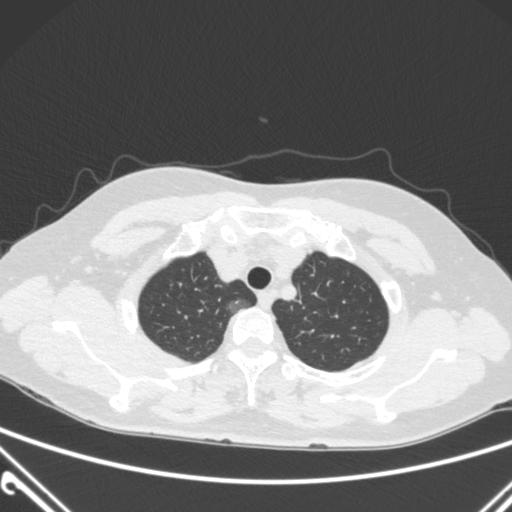
Chest CT, one axial slice. Slice 243 of 300 in the series (ordered by position). 120 kVp. Lung window (W 1500 / L -600 HU). 1 mm slice thickness. 512 × 512 image matrix, field of view 350 × 350 mm. Female patient, age 54 years. Case-level facts recorded for this patient, not image findings: clinical TNM (as recorded): T1a N0 M0; histopathological grade: G1.
Annotated regions visible in this slice (bounding box drawn by a radiologist):
- lung tumour (recorded histology: adenocarcinoma): bounding box <226,292,259,315> (left, top, right, bottom; pixels)